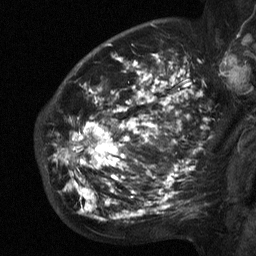
Breast MRI (dynamic contrast-enhanced), one sagittal slice. Slice 42 of 64 in the series (ordered by position). Dynamic contrast-enhanced study with each time point stored as its own series, time point 2 of 3 at this slice position (early post-contrast, ordered by acquisition time). 1.5 T. TE 4.8 ms, TR 27 ms. 2.3 mm slice thickness. 256 × 256 image matrix, field of view 200 × 200 mm. Patient: female, 50 years. Case-level facts recorded for this patient, not image findings: setting: breast cancer imaged before/during neoadjuvant chemotherapy; receptor status: HER2-positive.
Outlined on this slice (semi-automatic segmentation, software-assisted and operator-edited):
- analysis volume of interest (the breast-tissue region the enhancement analysis was run in; not a lesion): box from (x=53, y=64) to (x=211, y=218) px
- tumour enhancement mask (voxels above the 90 % enhancement threshold inside the analysis volume of interest): (x=54, y=64)–(x=201, y=218)